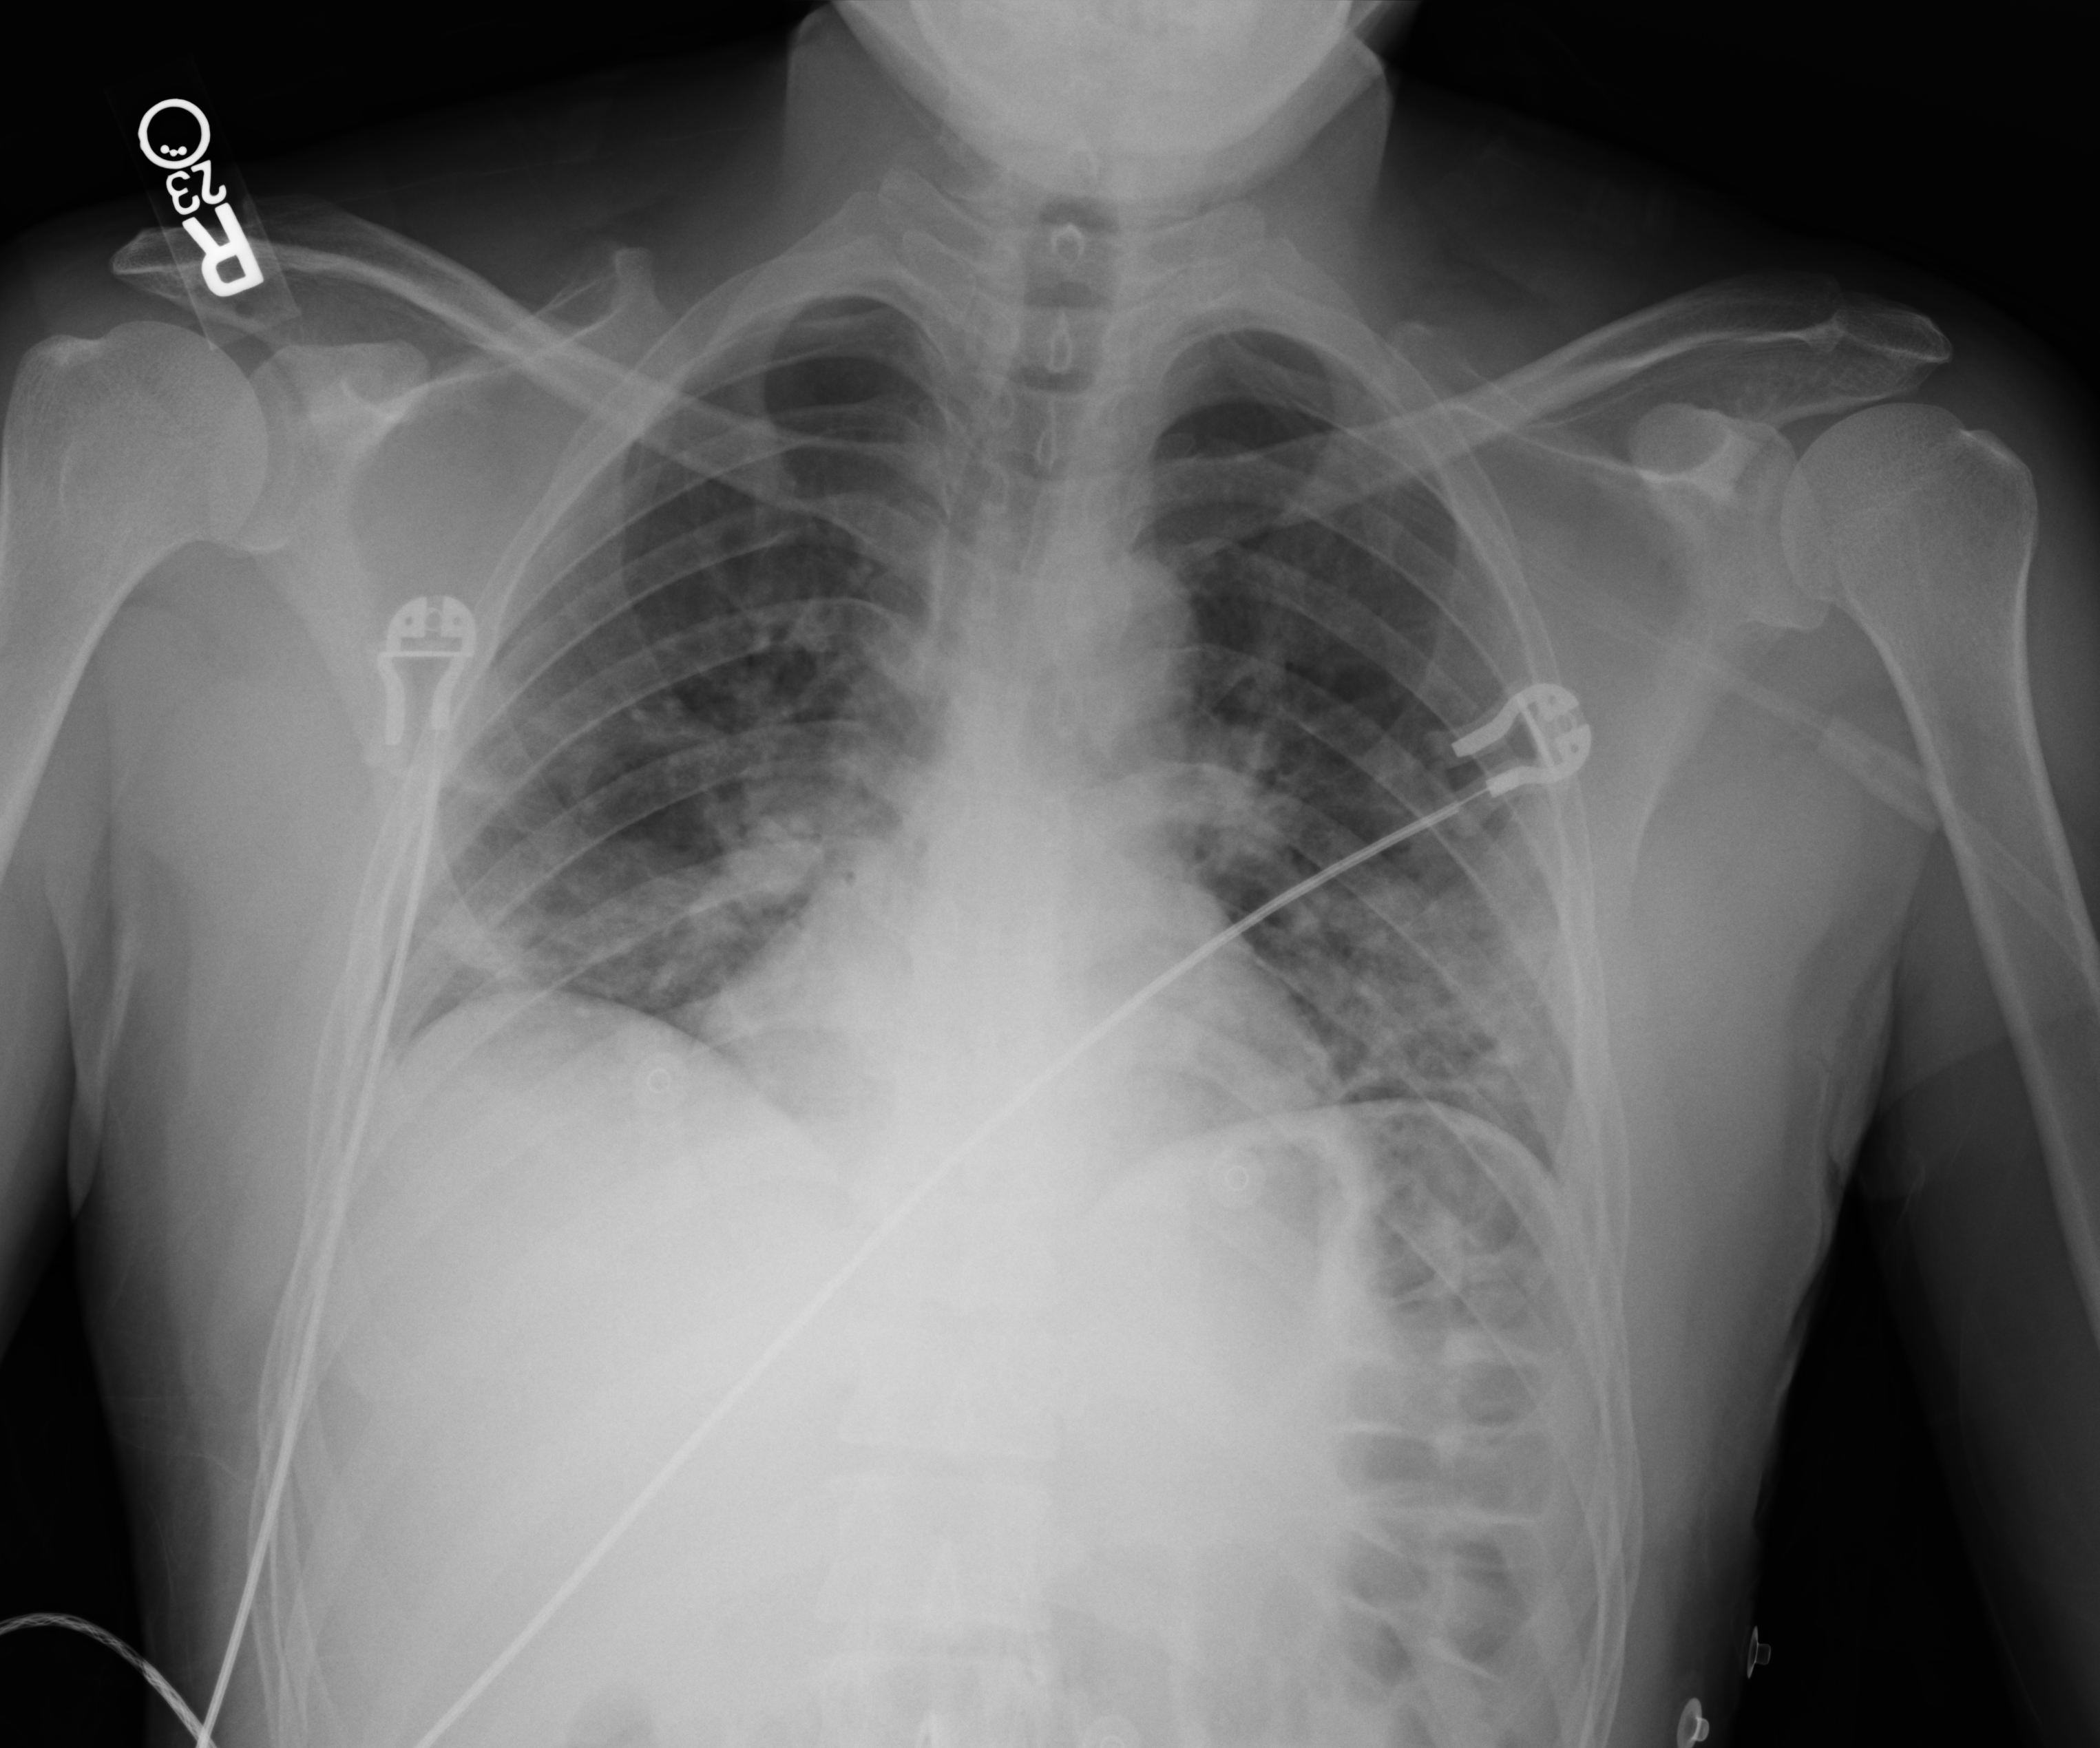
Bedside chest radiograph (computed radiography), anteroposterior (AP) projection. Patient hospitalised with COVID-19; male, aged 18–59 years.
Hospital-stay facts (about this admission, not read from this image; timing relative to this image not recorded): mechanically ventilated during this hospital stay: no; admitted to intensive care during this hospital stay: yes.